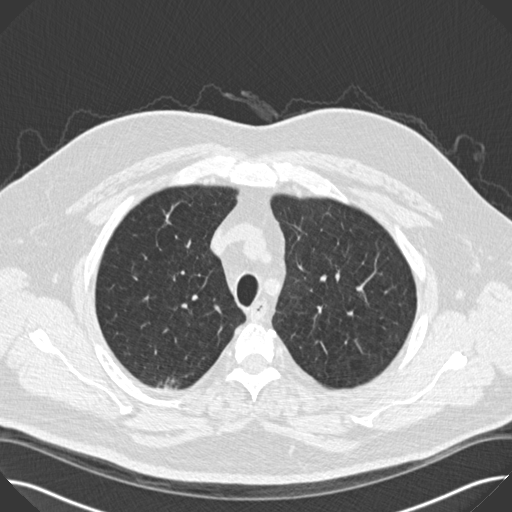
Chest CT (low-dose screening protocol), one axial image, baseline annual screen, lung window (W 1500 / L -600 HU), 2 mm slice thickness, slice 127 of 158 in the series. Male participant, aged 65 years at enrolment.
Expert-annotated lung lesion, bounding box <148,359,192,414> (left, top, right, bottom; pixels). The screening reader recorded 2 non-calcified nodules or masses ≥4 mm on this exam; which of them this box marks is not recorded. Participant outcome: lung cancer diagnosed 47 days after this screen — bronchiolo-alveolar adenocarcinoma, NOS, right upper lobe, moderately differentiated (G2), stage IIA (AJCC 6th edition), 14 mm at pathology.